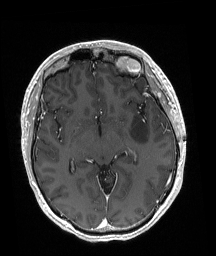
Brain MRI from a brain-tumour surgery series, one axial slice; position 109 of 192 along the scan axis; T1-weighted post-contrast; 1 mm slice thickness; 216 × 256 image matrix. Case-level facts recorded for this patient, not image findings: histopathology: Astrocytoma; WHO grade: 3; IDH mutation: yes.
Structures marked on this image (outlined manually by an expert reader):
- tumour: bounding box <131,114,147,142> (left, top, right, bottom; pixels)